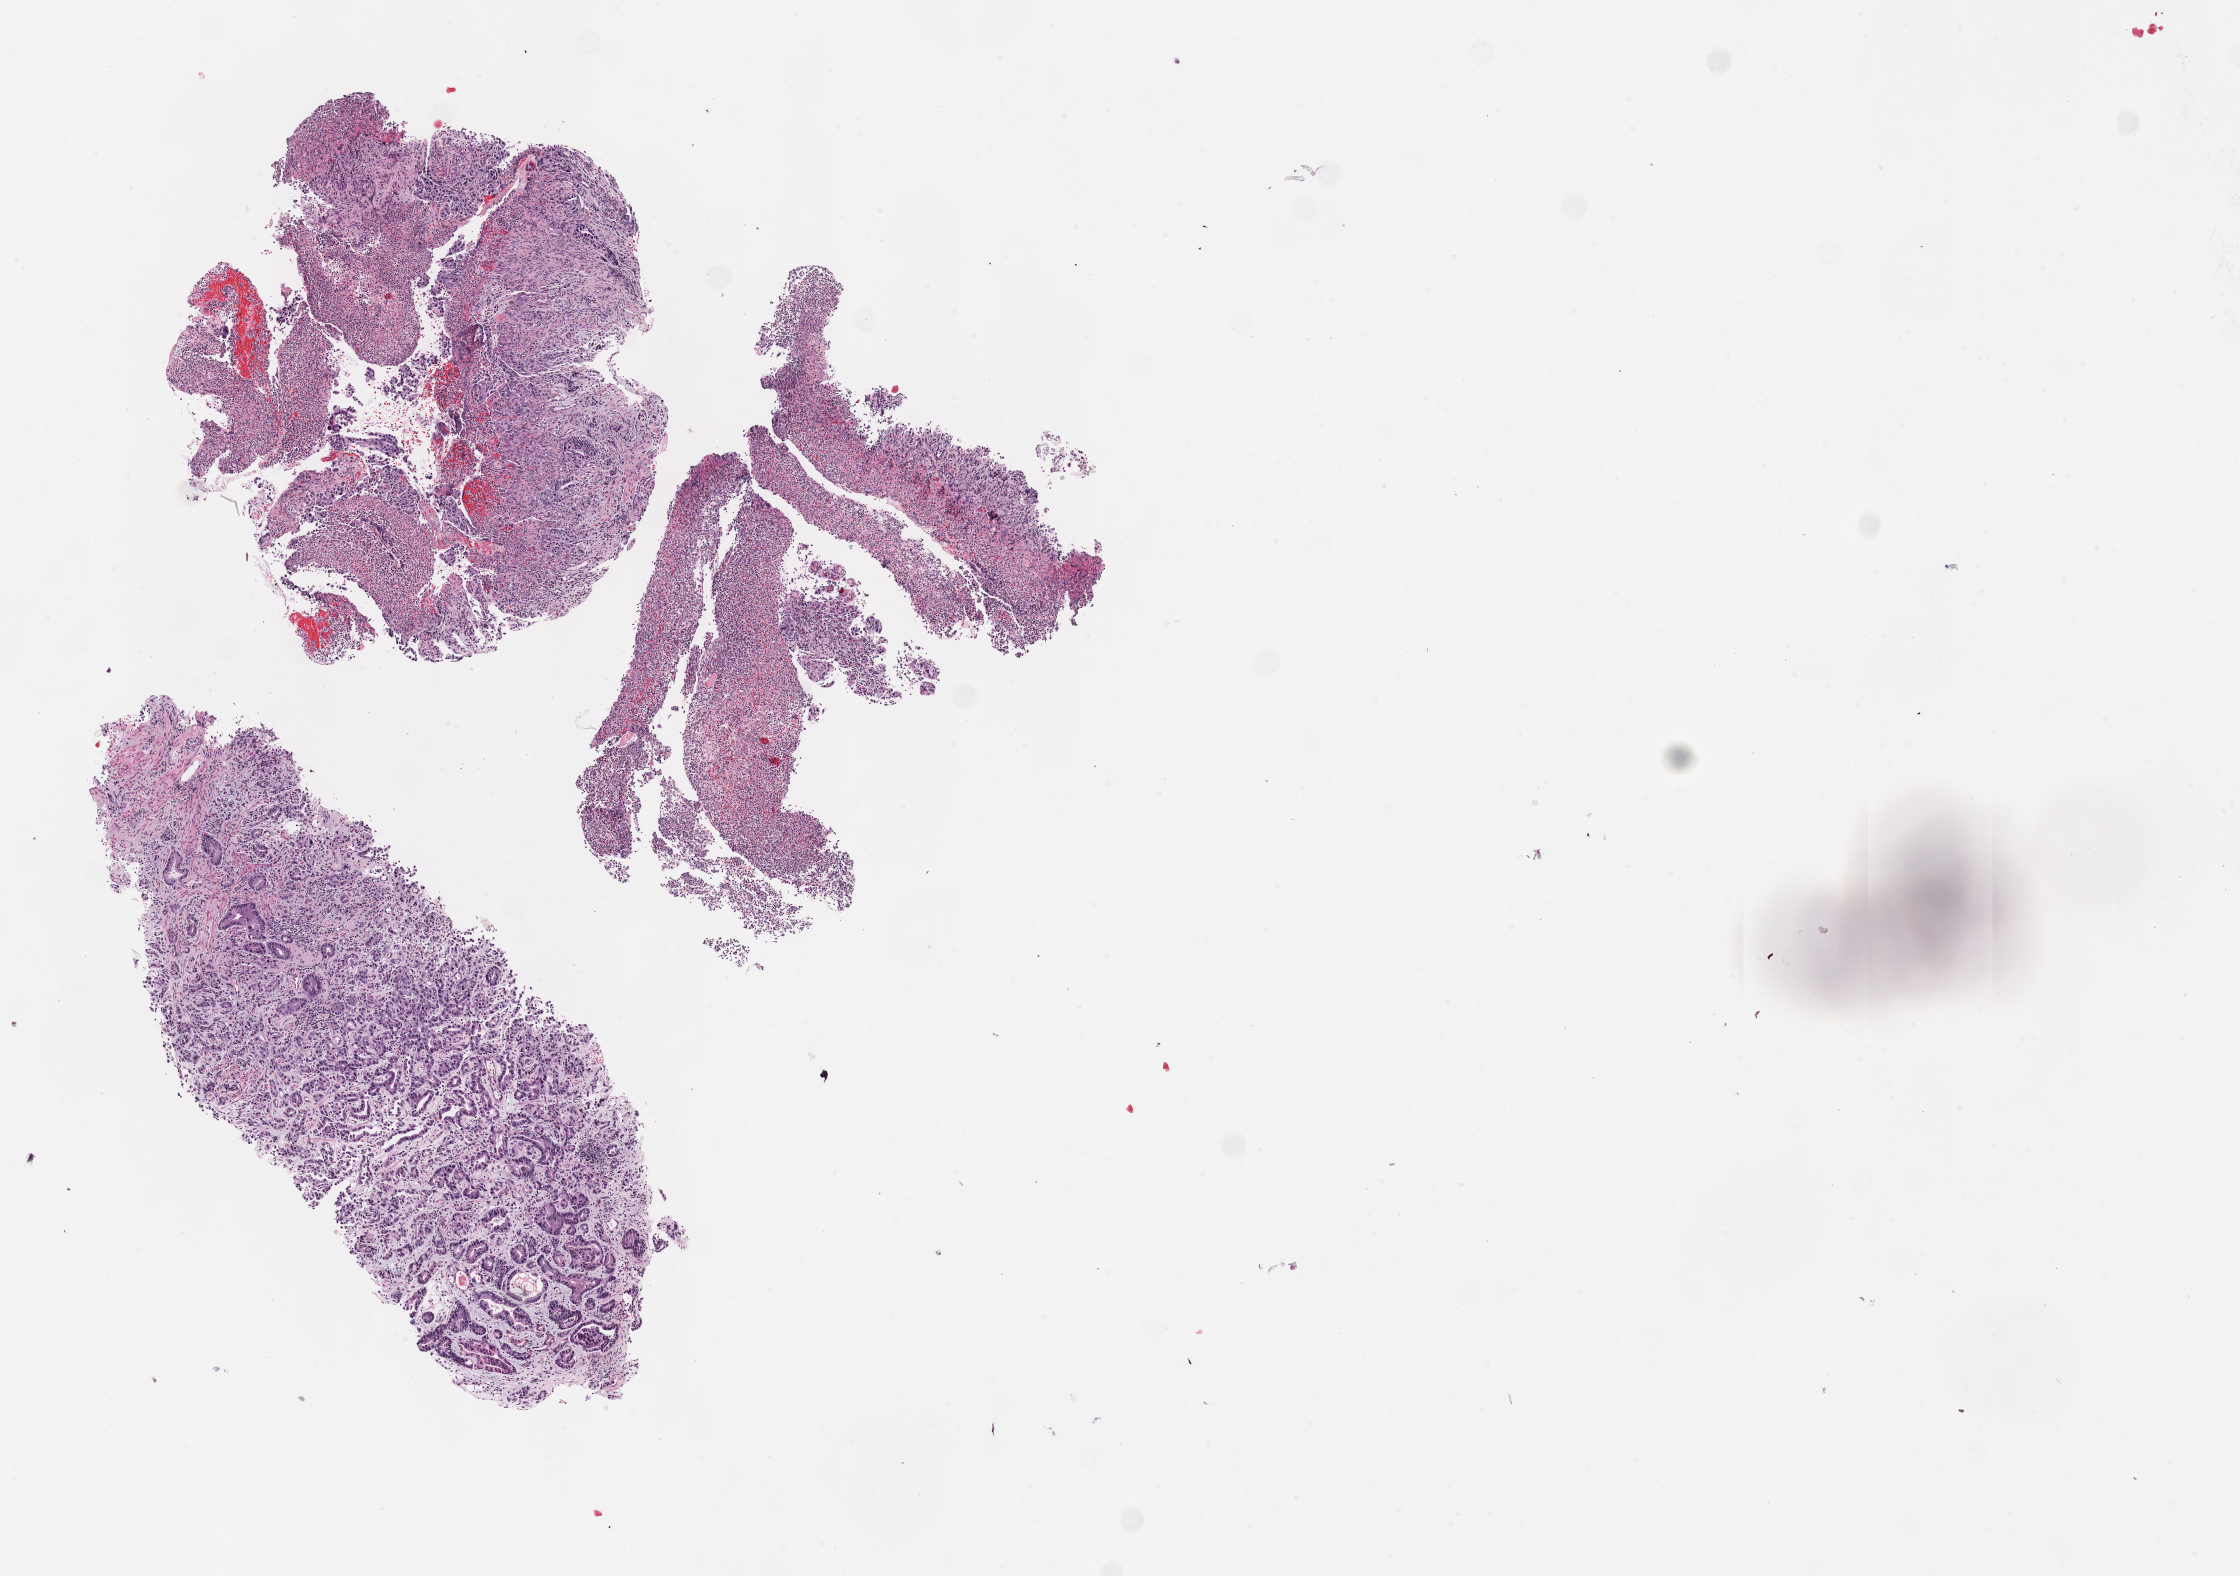
H&E whole-slide image — shown as a low-resolution overview of the whole scanned area (about 9.1 x 6.4 mm, acquisition: 40x scan). FFPE section. Primary tumour sample from the stomach. Male patient; age at initial diagnosis 66 years. Histologic grade: G3 (poorly differentiated).
TNM: T3 N0 M0. AJCC pathologic stage: IIA (7th edition). Lymph nodes positive (case pathology): 0 of 10 examined. Diagnosis: Adenocarcinoma, NOS.